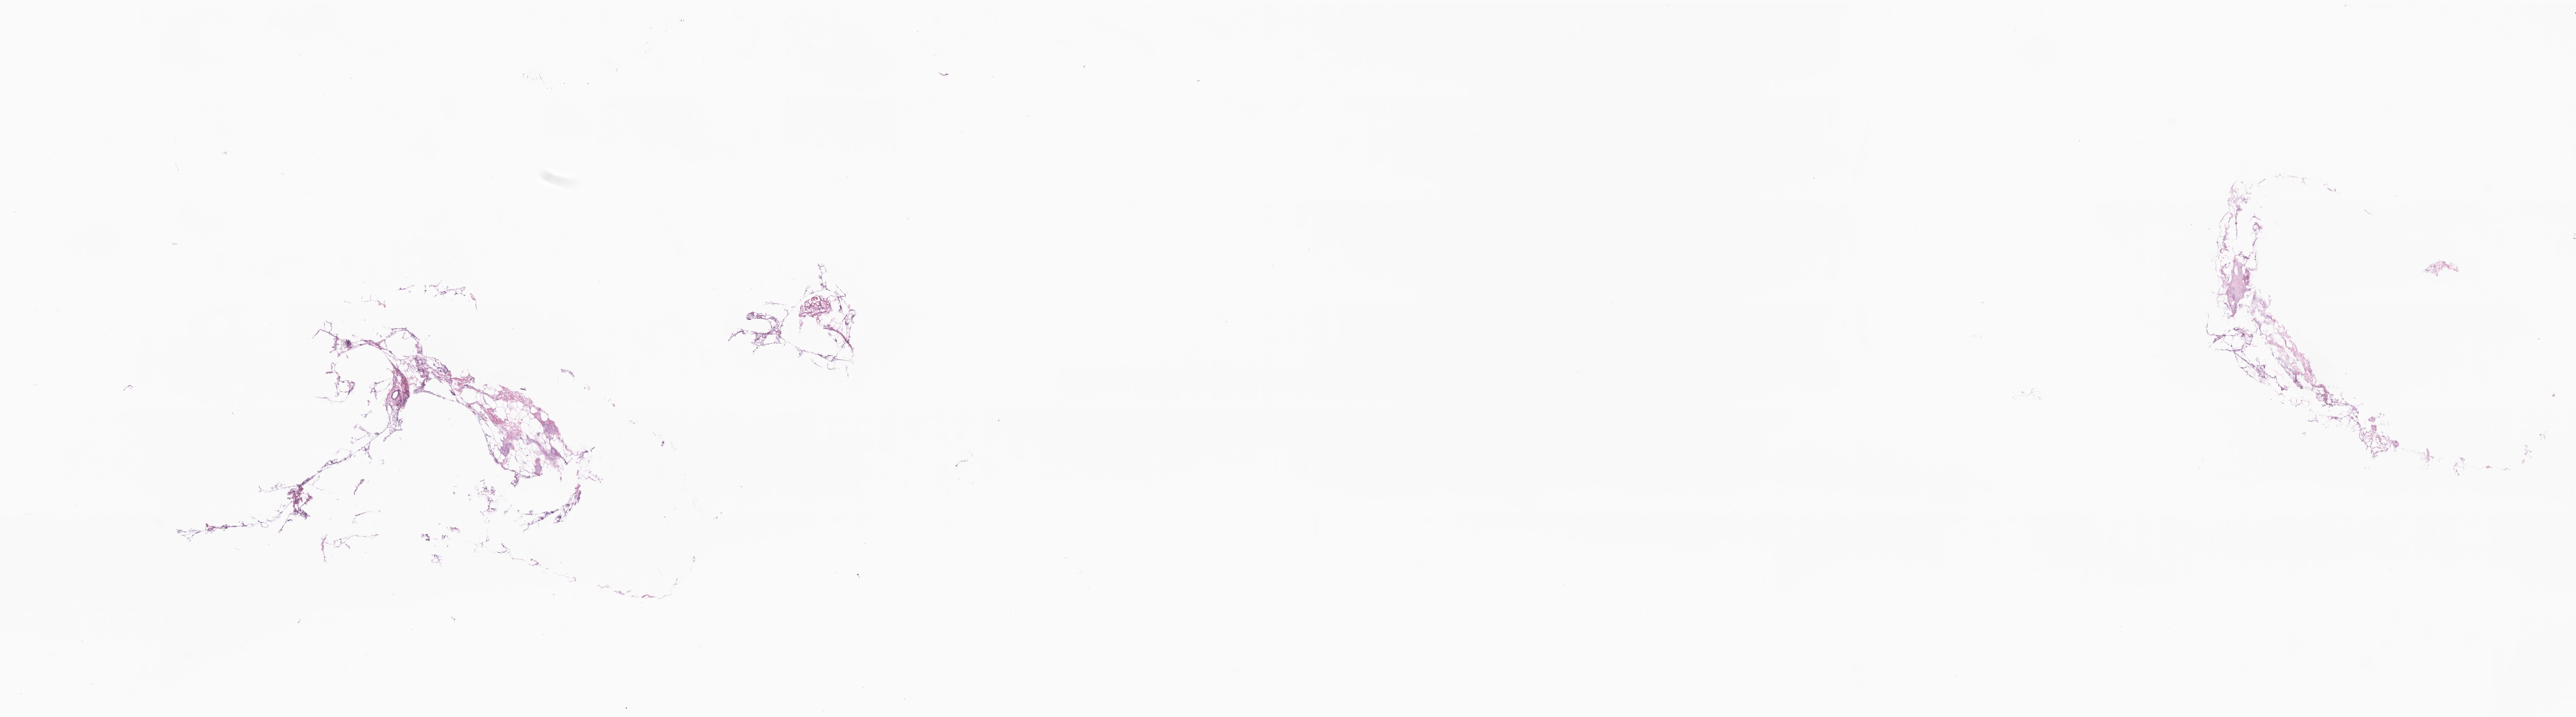
Whole-slide image, H&E stain — a low-resolution overview of the entire scanned area, about 26.5 x 7.4 mm; cryosection; specimen: primary tumor; anatomic site: breast (left). Patient: female, age at initial diagnosis 53 years.
Diagnosis: Infiltrating duct carcinoma, NOS.